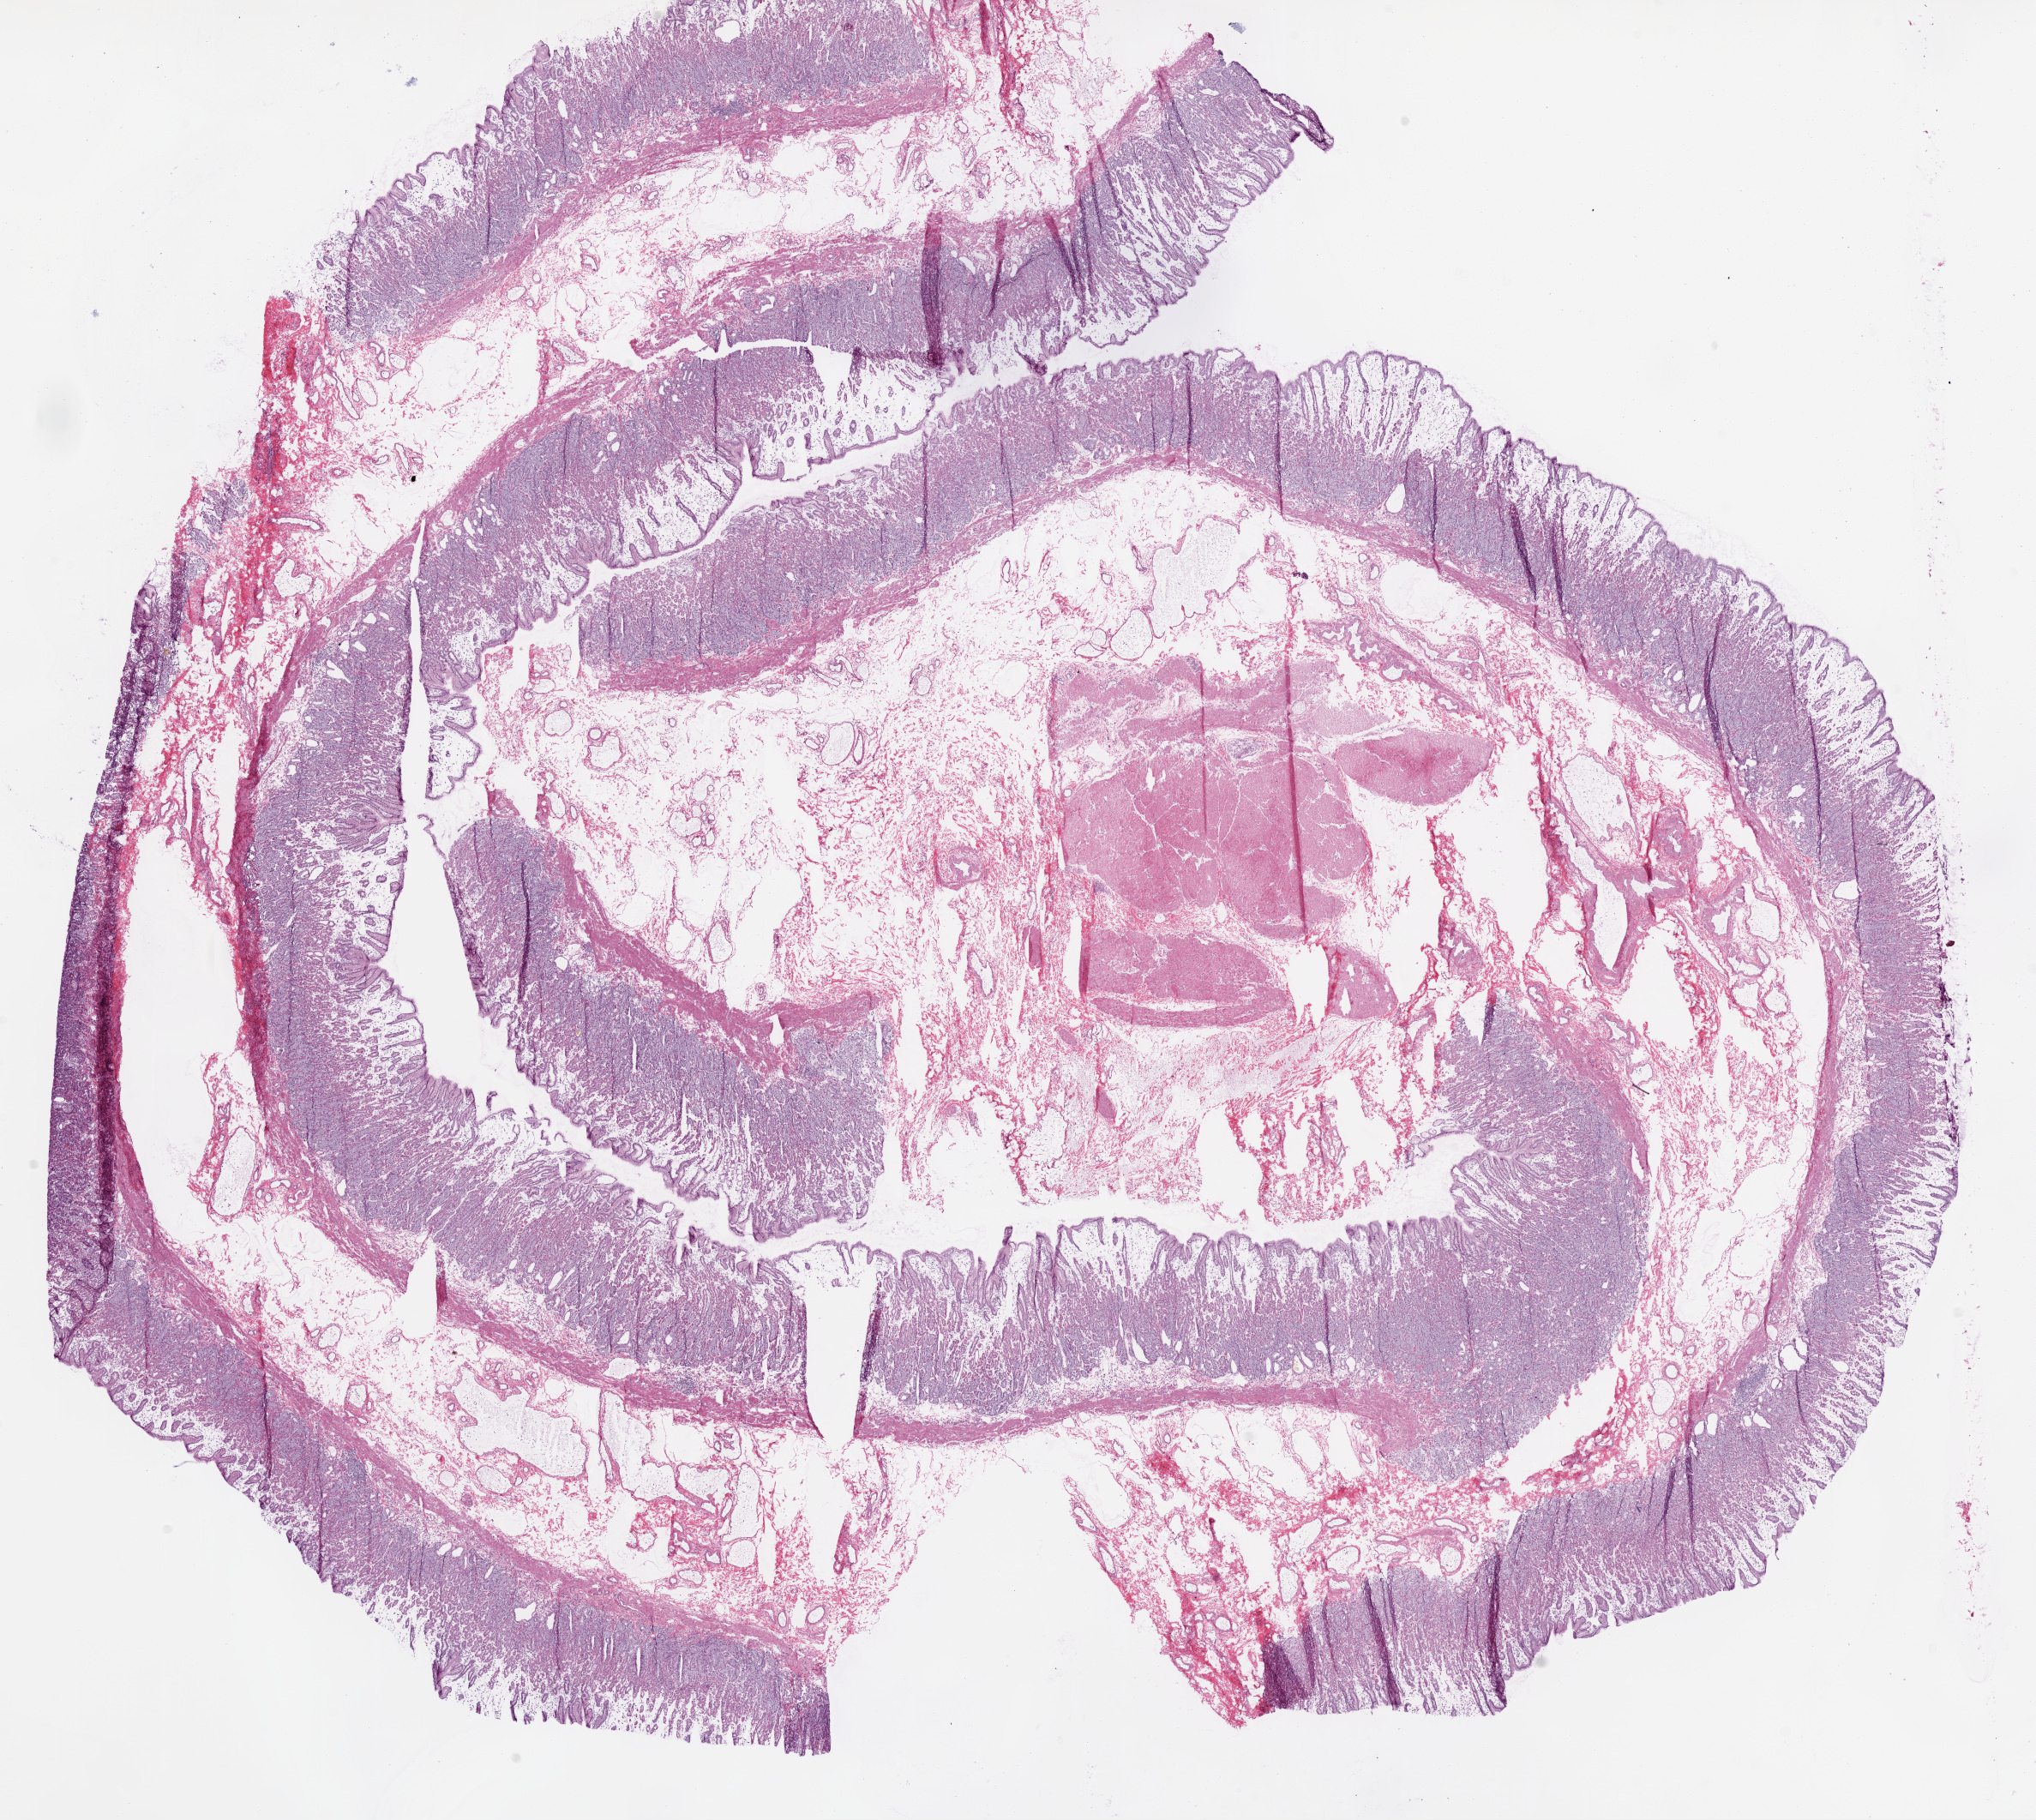
Digitized H&E-stained tissue section (whole slide) — low-resolution overview of the scanned area, about 19.1 x 17.0 mm; frozen section from the bottom of the tissue portion; solid tissue normal (non-tumour tissue) sample from the stomach. Female patient; age at initial diagnosis 55 years.
This section: solid tissue normal sample (biorepository sample class). Patient diagnosis: Adenocarcinoma, NOS (cardia, NOS).